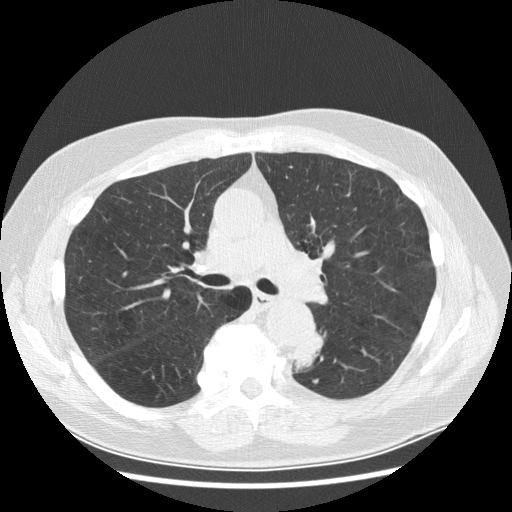
Axial slice from a low-dose chest CT screening exam; baseline annual screen; lung window (W 1500 / L -600 HU); 2.5 mm slice thickness; standard (soft-tissue) reconstruction kernel (STANDARD); slice 106 of 282 in the series. Male, age 70 years at enrolment.
Expert-annotated lung lesion, bounding box <278,328,329,383> (left, top, right, bottom; pixels). Reader record for this screening exam (exam-level; its link to the box is not recorded): non-calcified nodule or mass ≥4 mm, left lower lobe, 27 × 16 mm, spiculated (stellate) margins, soft tissue attenuation, pre-existing on the prior screen: yes; interval growth: yes. Later outcome: lung cancer diagnosed 97 days after this screen — papillary adenocarcinoma, NOS, left lower lobe, moderately differentiated (G2), stage IB (AJCC 6th edition), 35 mm at pathology.